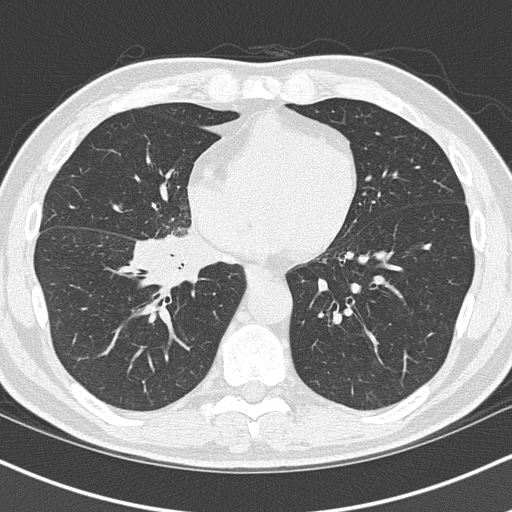
Chest CT (low-dose screening protocol), one axial image. Baseline screening round. Lung window (W 1500 / L -600 HU). Lung (sharp) reconstruction kernel (B50f). Slice 51 of 151 in the series. 512 × 512 image matrix, field of view 320 × 320 mm. Male, age 55 years at enrolment.
• Expert-annotated lung lesion, bounding box [x1, y1, x2, y2] px = [130, 225, 240, 308].
• Reader record for this screening exam (exam-level; its link to the box is not recorded): non-calcified nodule or mass ≥4 mm, right lower lobe, 6 × 5 mm, spiculated (stellate) margins, soft tissue attenuation.
• Lung cancer was diagnosed 21 days after this screen: carcinoma, NOS, right hilum, stage IB (AJCC 6th edition), 67 mm at pathology.